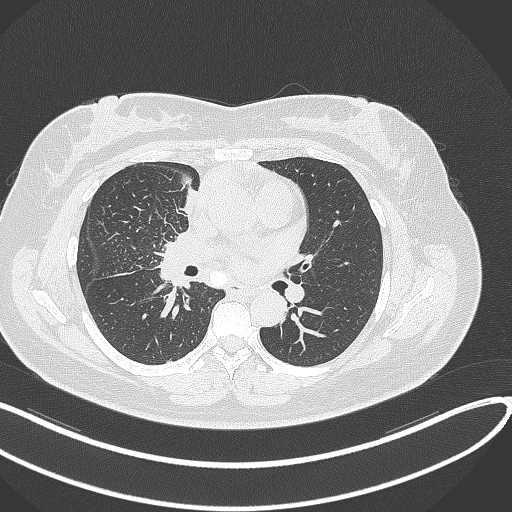
Chest CT, one axial slice; slice 142 of 303 in the series (ordered by position); reconstruction kernel B70f; 120 kVp; lung window (W 1500 / L -600 HU); 1 mm slice thickness; 512 × 512 image matrix, field of view 400 × 400 mm. Female patient, age 46 years. Case-level facts recorded for this patient, not image findings: clinical TNM (as recorded): T2a N1 M0.
Outlined on this slice (rectangle marked by the reading radiologist):
- lung tumour (recorded histology: adenocarcinoma): bounding box <175,188,201,218> (left, top, right, bottom; pixels)